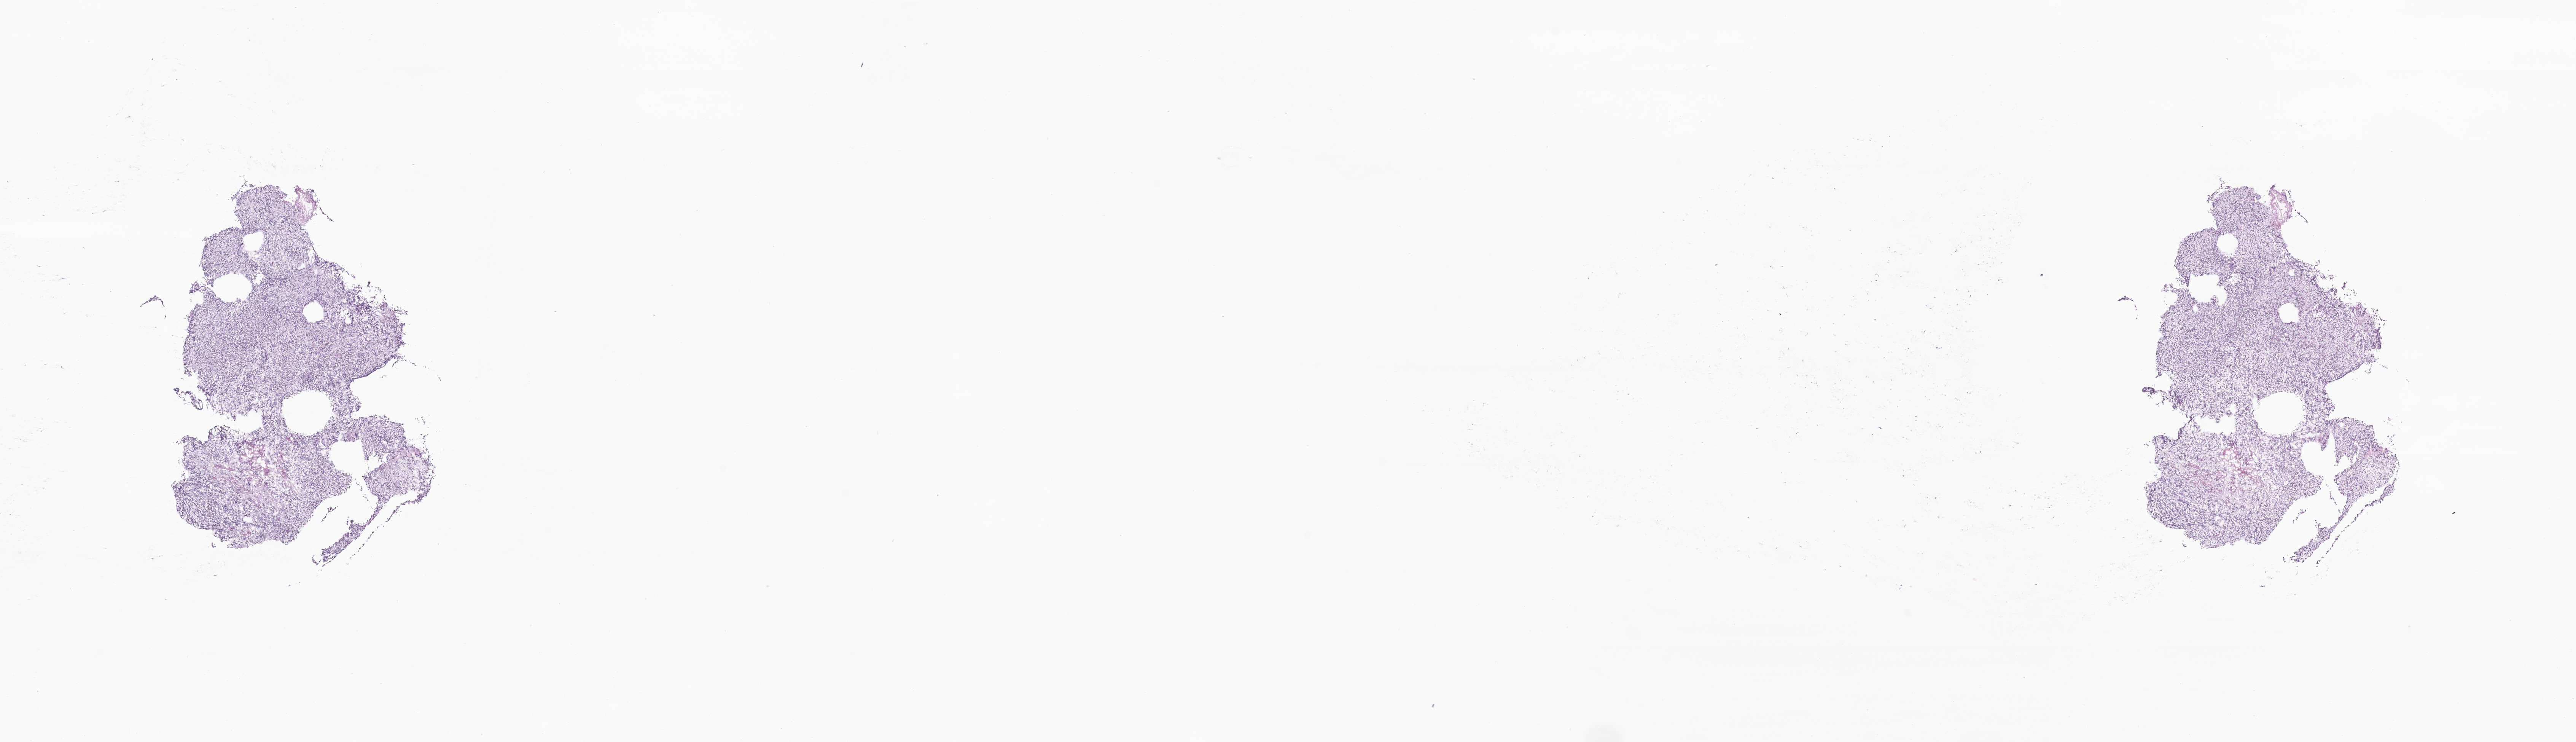
Digitized haematoxylin and eosin-stained section of tumor tissue from the brain, whole scanned area (about 28.5 x 8.2 mm) shown as a low-resolution overview; frozen section. Patient: male, age 74 months.
Diagnosis (ICD-O-3 morphology term): Medulloblastoma, NOS.